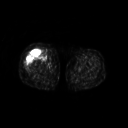
FDG PET of an extremity soft-tissue mass (from a PET/CT study), one axial slice; slice 229 of 311 in the series (ordered by position); 3.27 mm slice thickness; 128 × 128 image matrix, field of view 500 × 500 mm. Female patient, age 57 years. Case-level facts recorded for this patient, not image findings: histological type: pleiomorphic undifferentiated sarcoma; grade: high; site of the primary tumour: right quadricep.
Outlined on this slice (expert contour drawn on MRI and transferred to this co-registered scan by the dataset authors):
- tumour plus oedema (research contour): bounding box [x1, y1, x2, y2] px = [25, 50, 45, 69]